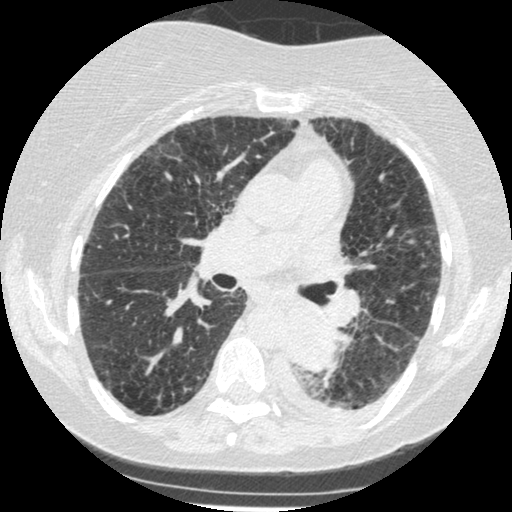
Axial slice from a low-dose chest CT screening exam. Third annual screen. Lung window (W 1500 / L -600 HU). 1.25 mm slice thickness. Standard (soft-tissue) reconstruction kernel (STANDARD). 120 kVp. 512 × 512 image matrix. Female participant, aged 60 years at enrolment. Former smoker at enrolment.
• Expert reader's lesion annotation, bounding box [x1, y1, x2, y2] px = [271, 307, 342, 374].
• The exam's reader record, not a measurement of the box and not confirmed to be the same lesion: non-calcified nodule or mass ≥4 mm, left lower lobe, 54 × 38 mm, smooth margins, soft tissue attenuation, pre-existing on the prior screen: yes; interval growth: yes.
• Official screen result: positive, other.